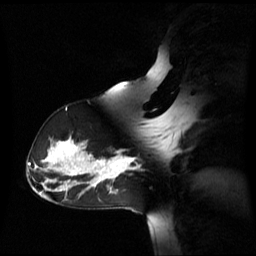
Breast MRI (dynamic contrast-enhanced), one sagittal slice. Slice 40 of 60 in the series (ordered by position). Dynamic contrast-enhanced series, image 2 of 3 at this slice position (ordered by acquisition). 1.5 T. TE 4.2 ms, TR 8.4 ms. 256 × 256 image matrix, field of view 270 × 270 mm. Female patient, age 39 years. Case-level facts recorded for this patient, not image findings: setting: breast cancer imaged before/during neoadjuvant chemotherapy; receptor status: triple-negative.
Annotated regions visible in this slice (semi-automatic segmentation, software-assisted and operator-edited):
- analysis volume of interest (the breast-tissue region the enhancement analysis was run in; not a lesion): bounding box (x1, y1, x2, y2) in pixels: (105, 157, 135, 179)
- tumour enhancement mask (voxels above the 70 % enhancement threshold inside the analysis volume of interest): (105, 157, 135, 179)